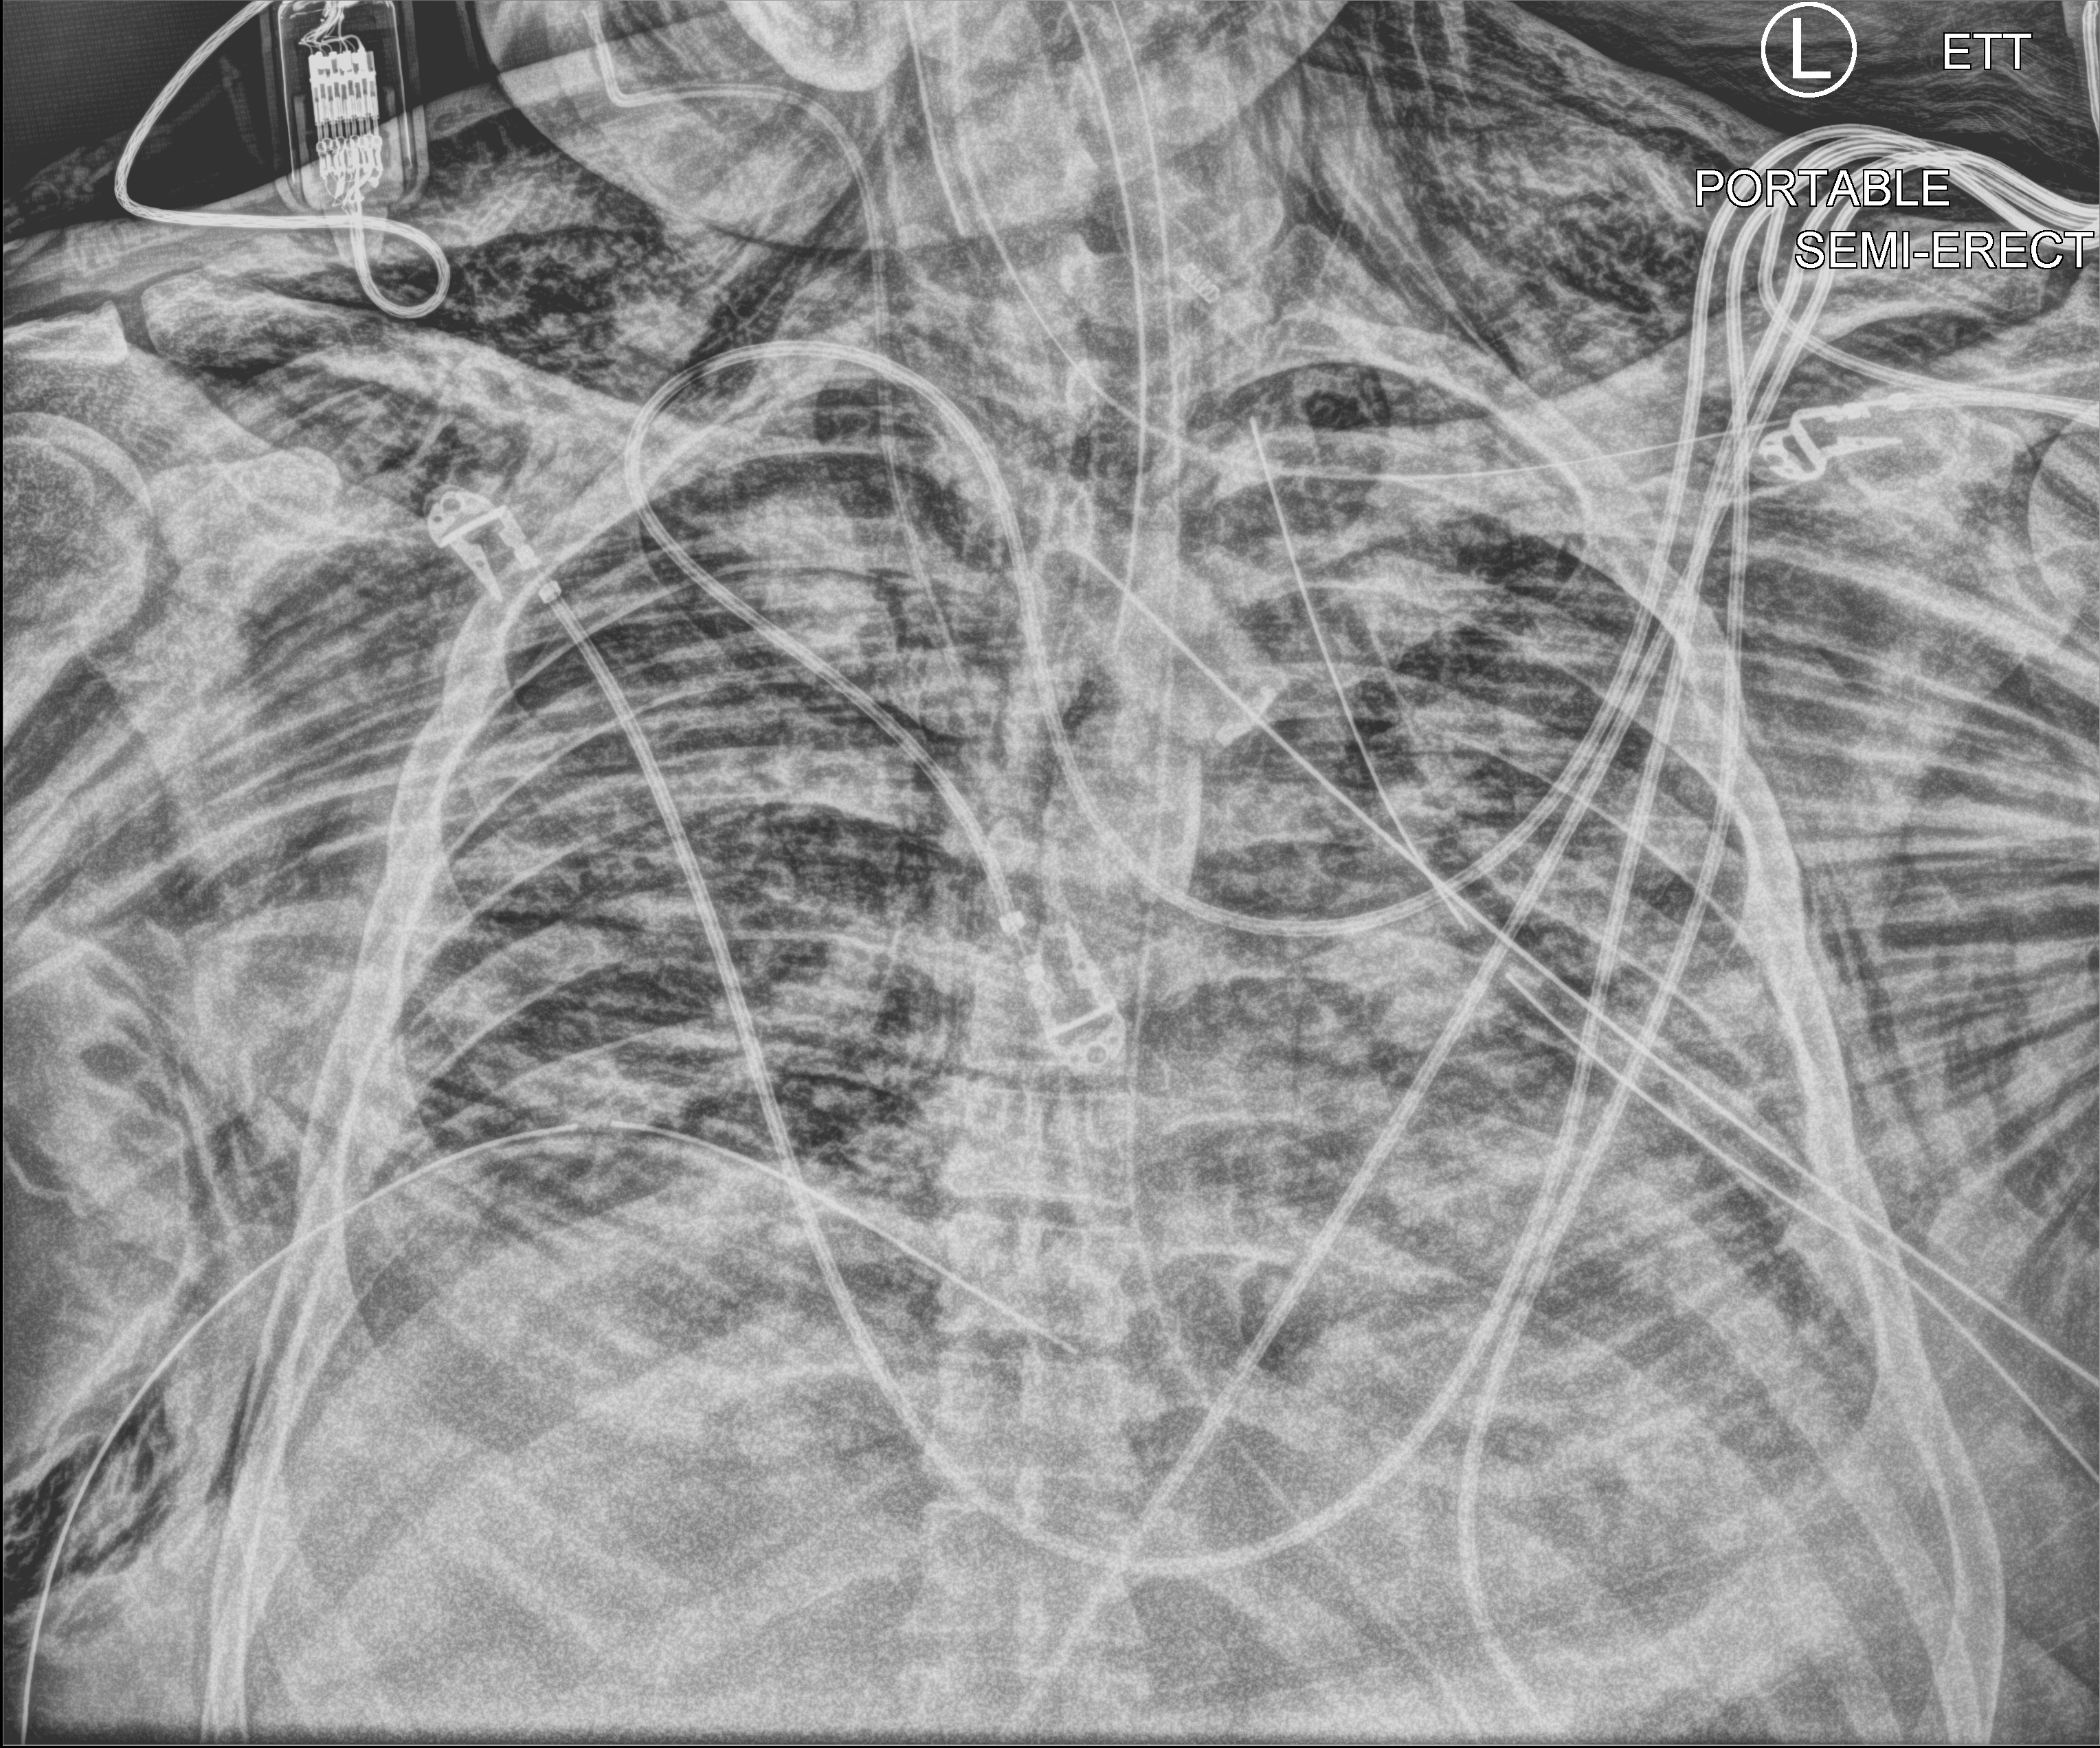
Portable chest radiograph; anteroposterior (AP) projection. Patient hospitalised with COVID-19; male, aged 18–59 years.
Hospital-stay facts (about this admission, not read from this image; timing relative to this image not recorded): mechanically ventilated during this hospital stay: yes.